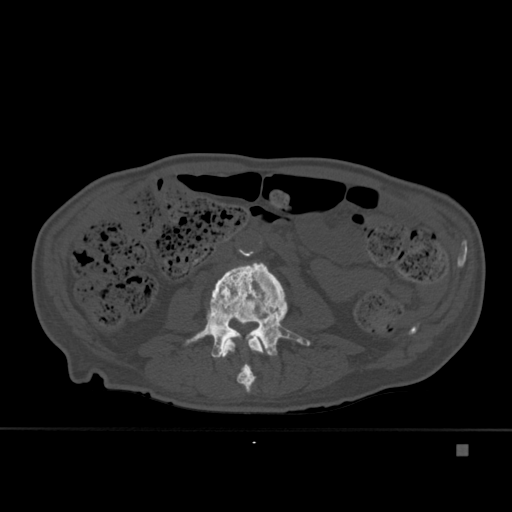
CT including the spine, one axial slice. Position 146 of 451 along the scan axis. Bone window (W 1800 / L 400 HU). 1.5 mm slice thickness. 512 × 512 image matrix, field of view 378 × 378 mm. Patient: male, 75 years. From the clinical record (not read from this slice): primary cancer: prostate.
Structures marked on this image (semi-automatically segmented with operator editing):
- L2 vertebra: bounding box [x1, y1, x2, y2] px = [223, 335, 264, 393]
- L3 vertebra: [185, 262, 311, 383]